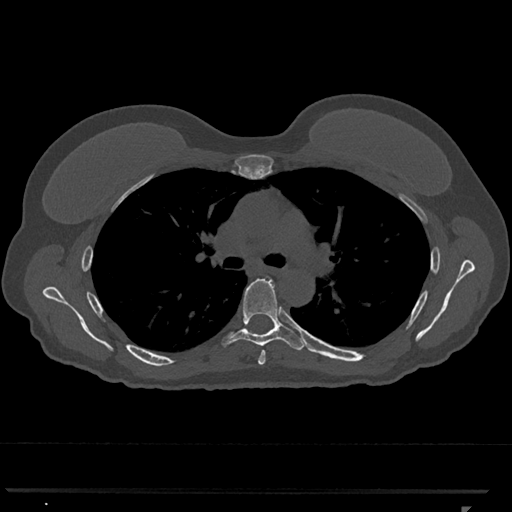
CT including the spine, one axial slice; position 768 of 793 along the scan axis; reconstruction kernel Br40s/3; bone window (W 1800 / L 400 HU); 0.5 mm slice thickness; 512 × 512 image matrix, field of view 380 × 380 mm. Patient: female, 62 years. Case-level facts recorded for this patient, not image findings: primary cancer: renal.
Annotated regions visible in this slice (semi-automatically segmented with operator editing):
- T5 vertebra: box from (x=258, y=351) to (x=266, y=365) px
- T6 vertebra: (x=222, y=279)–(x=304, y=351)